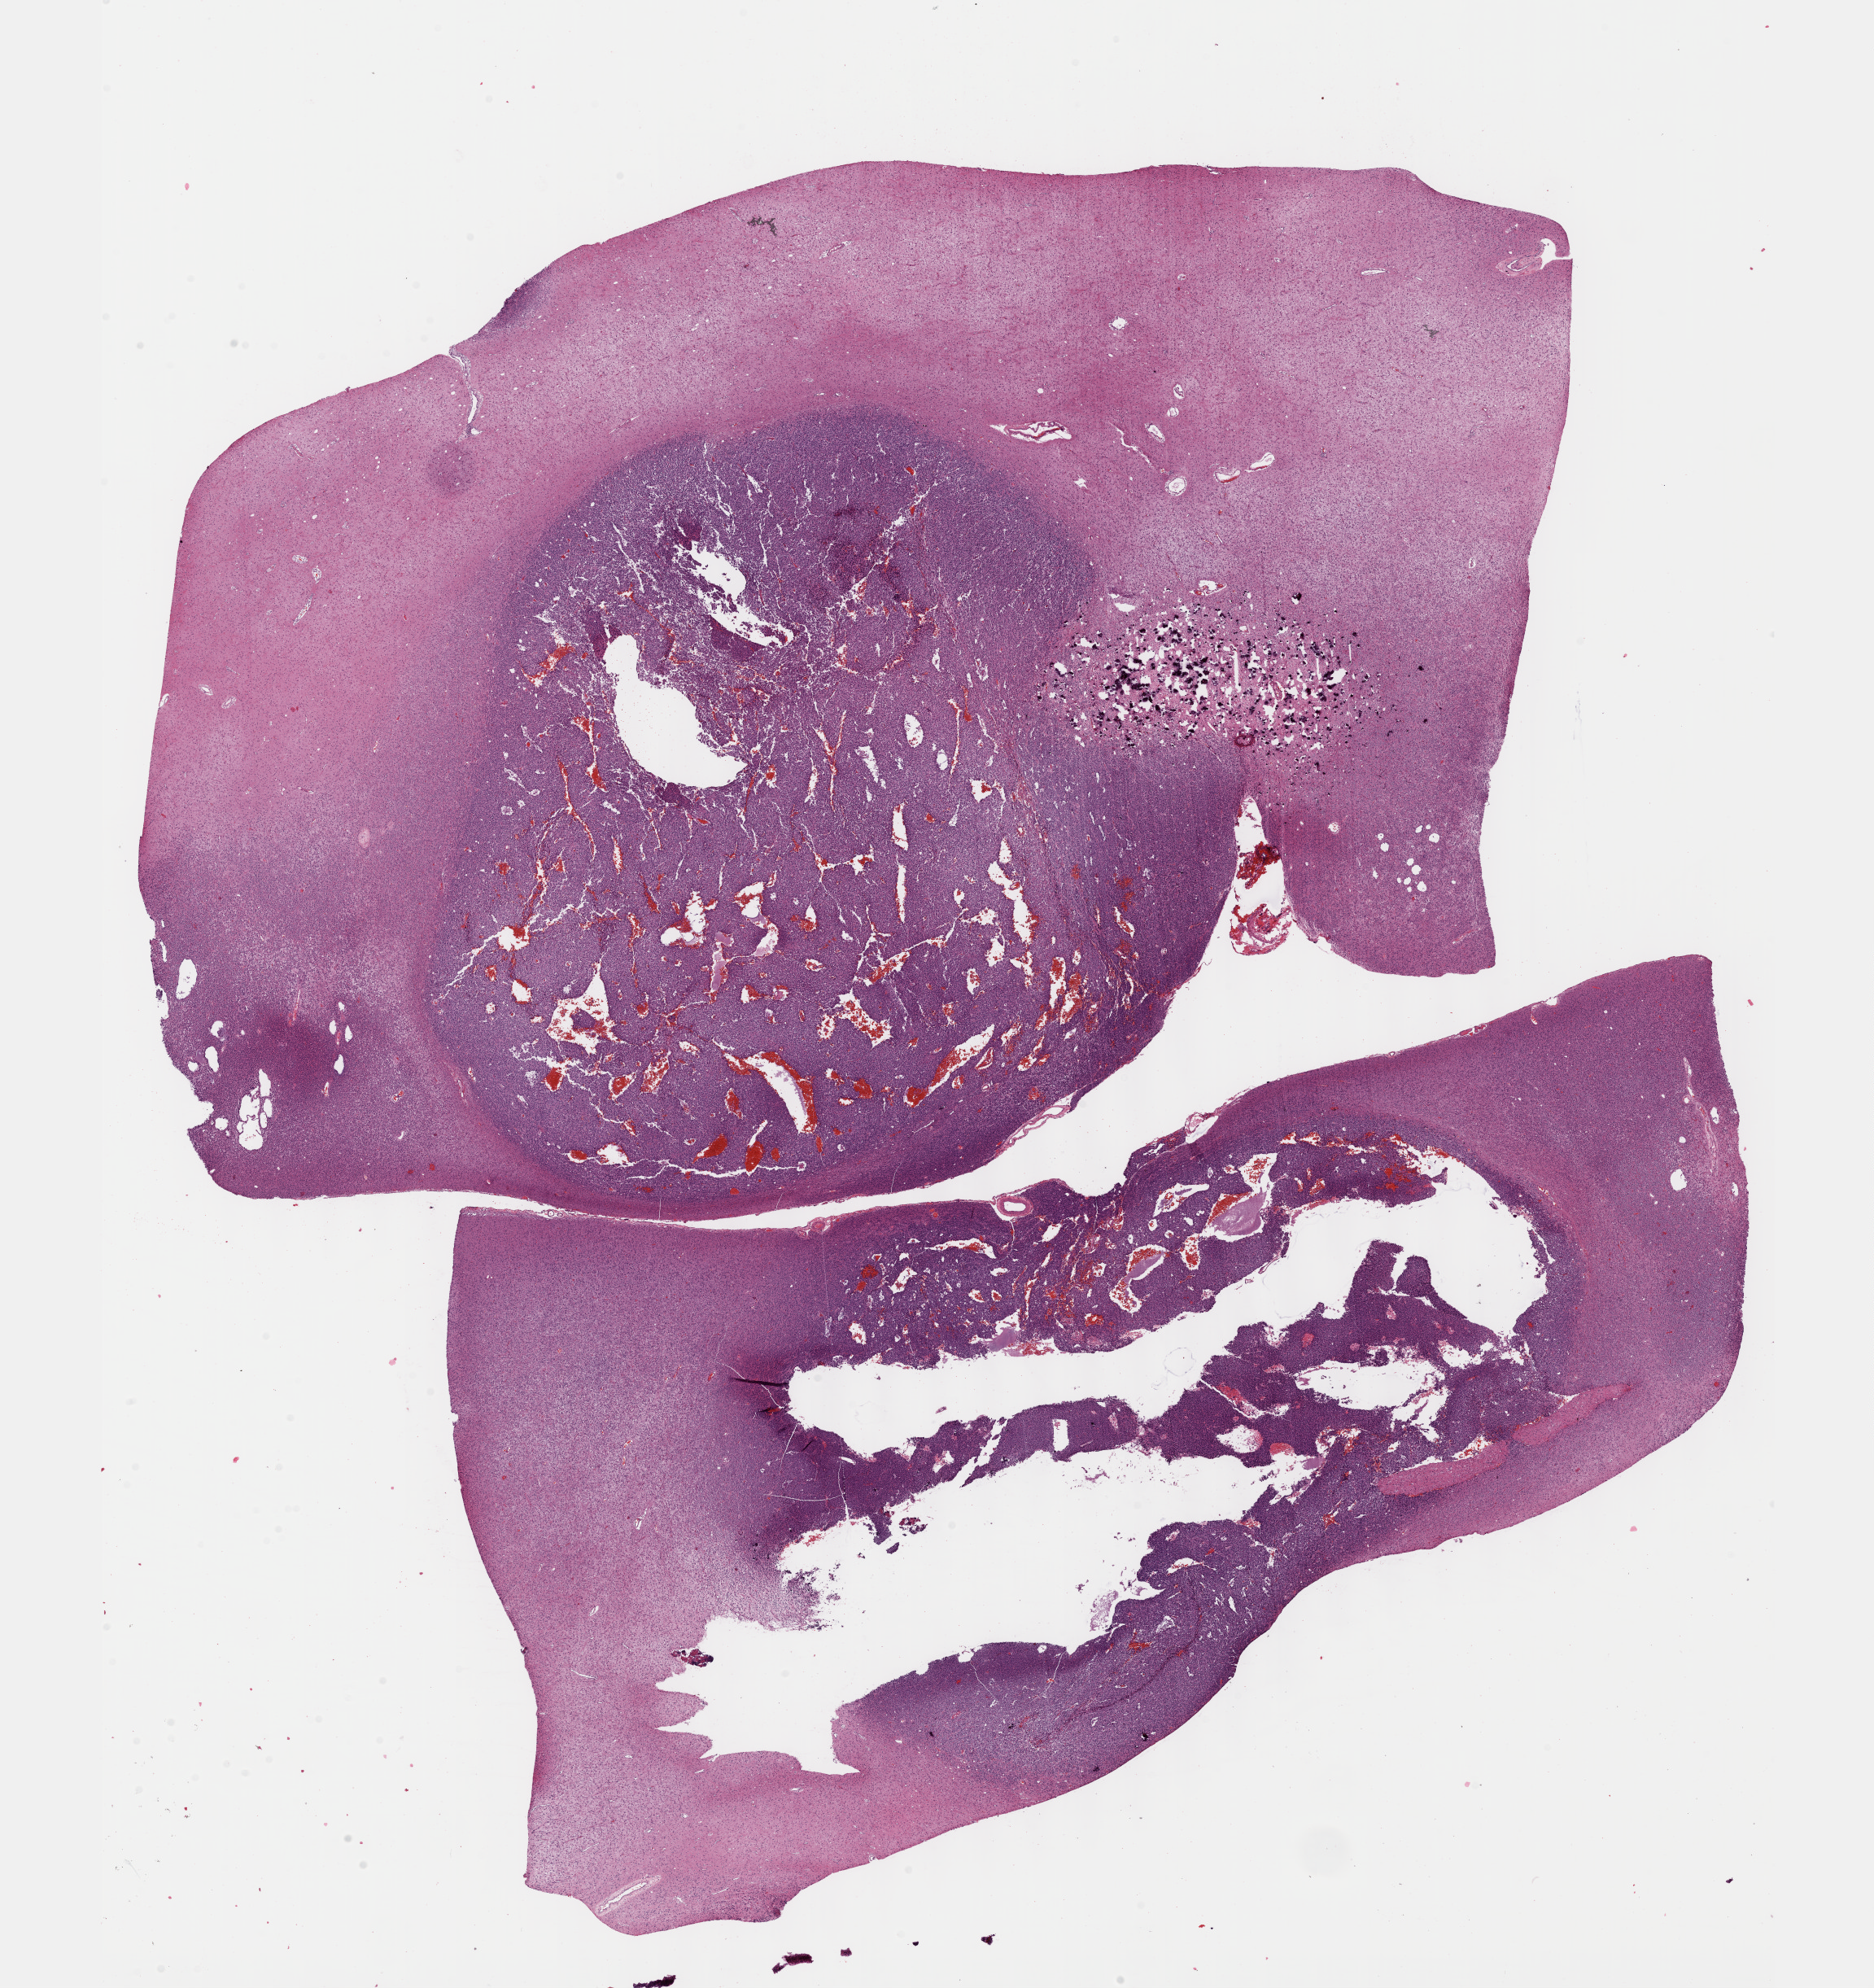
Digitized H&E-stained tissue section (whole slide) — shown as a low-resolution overview of the whole scanned area (about 18.6 x 19.7 mm, from a 40x scan). Formalin-fixed paraffin-embedded (FFPE) diagnostic section. Sample: primary tumour, brain. Female, age 41 years at initial diagnosis. Histologic grade: G3 (poorly differentiated).
Laterality: right. Diagnosis: Oligodendroglioma, anaplastic.